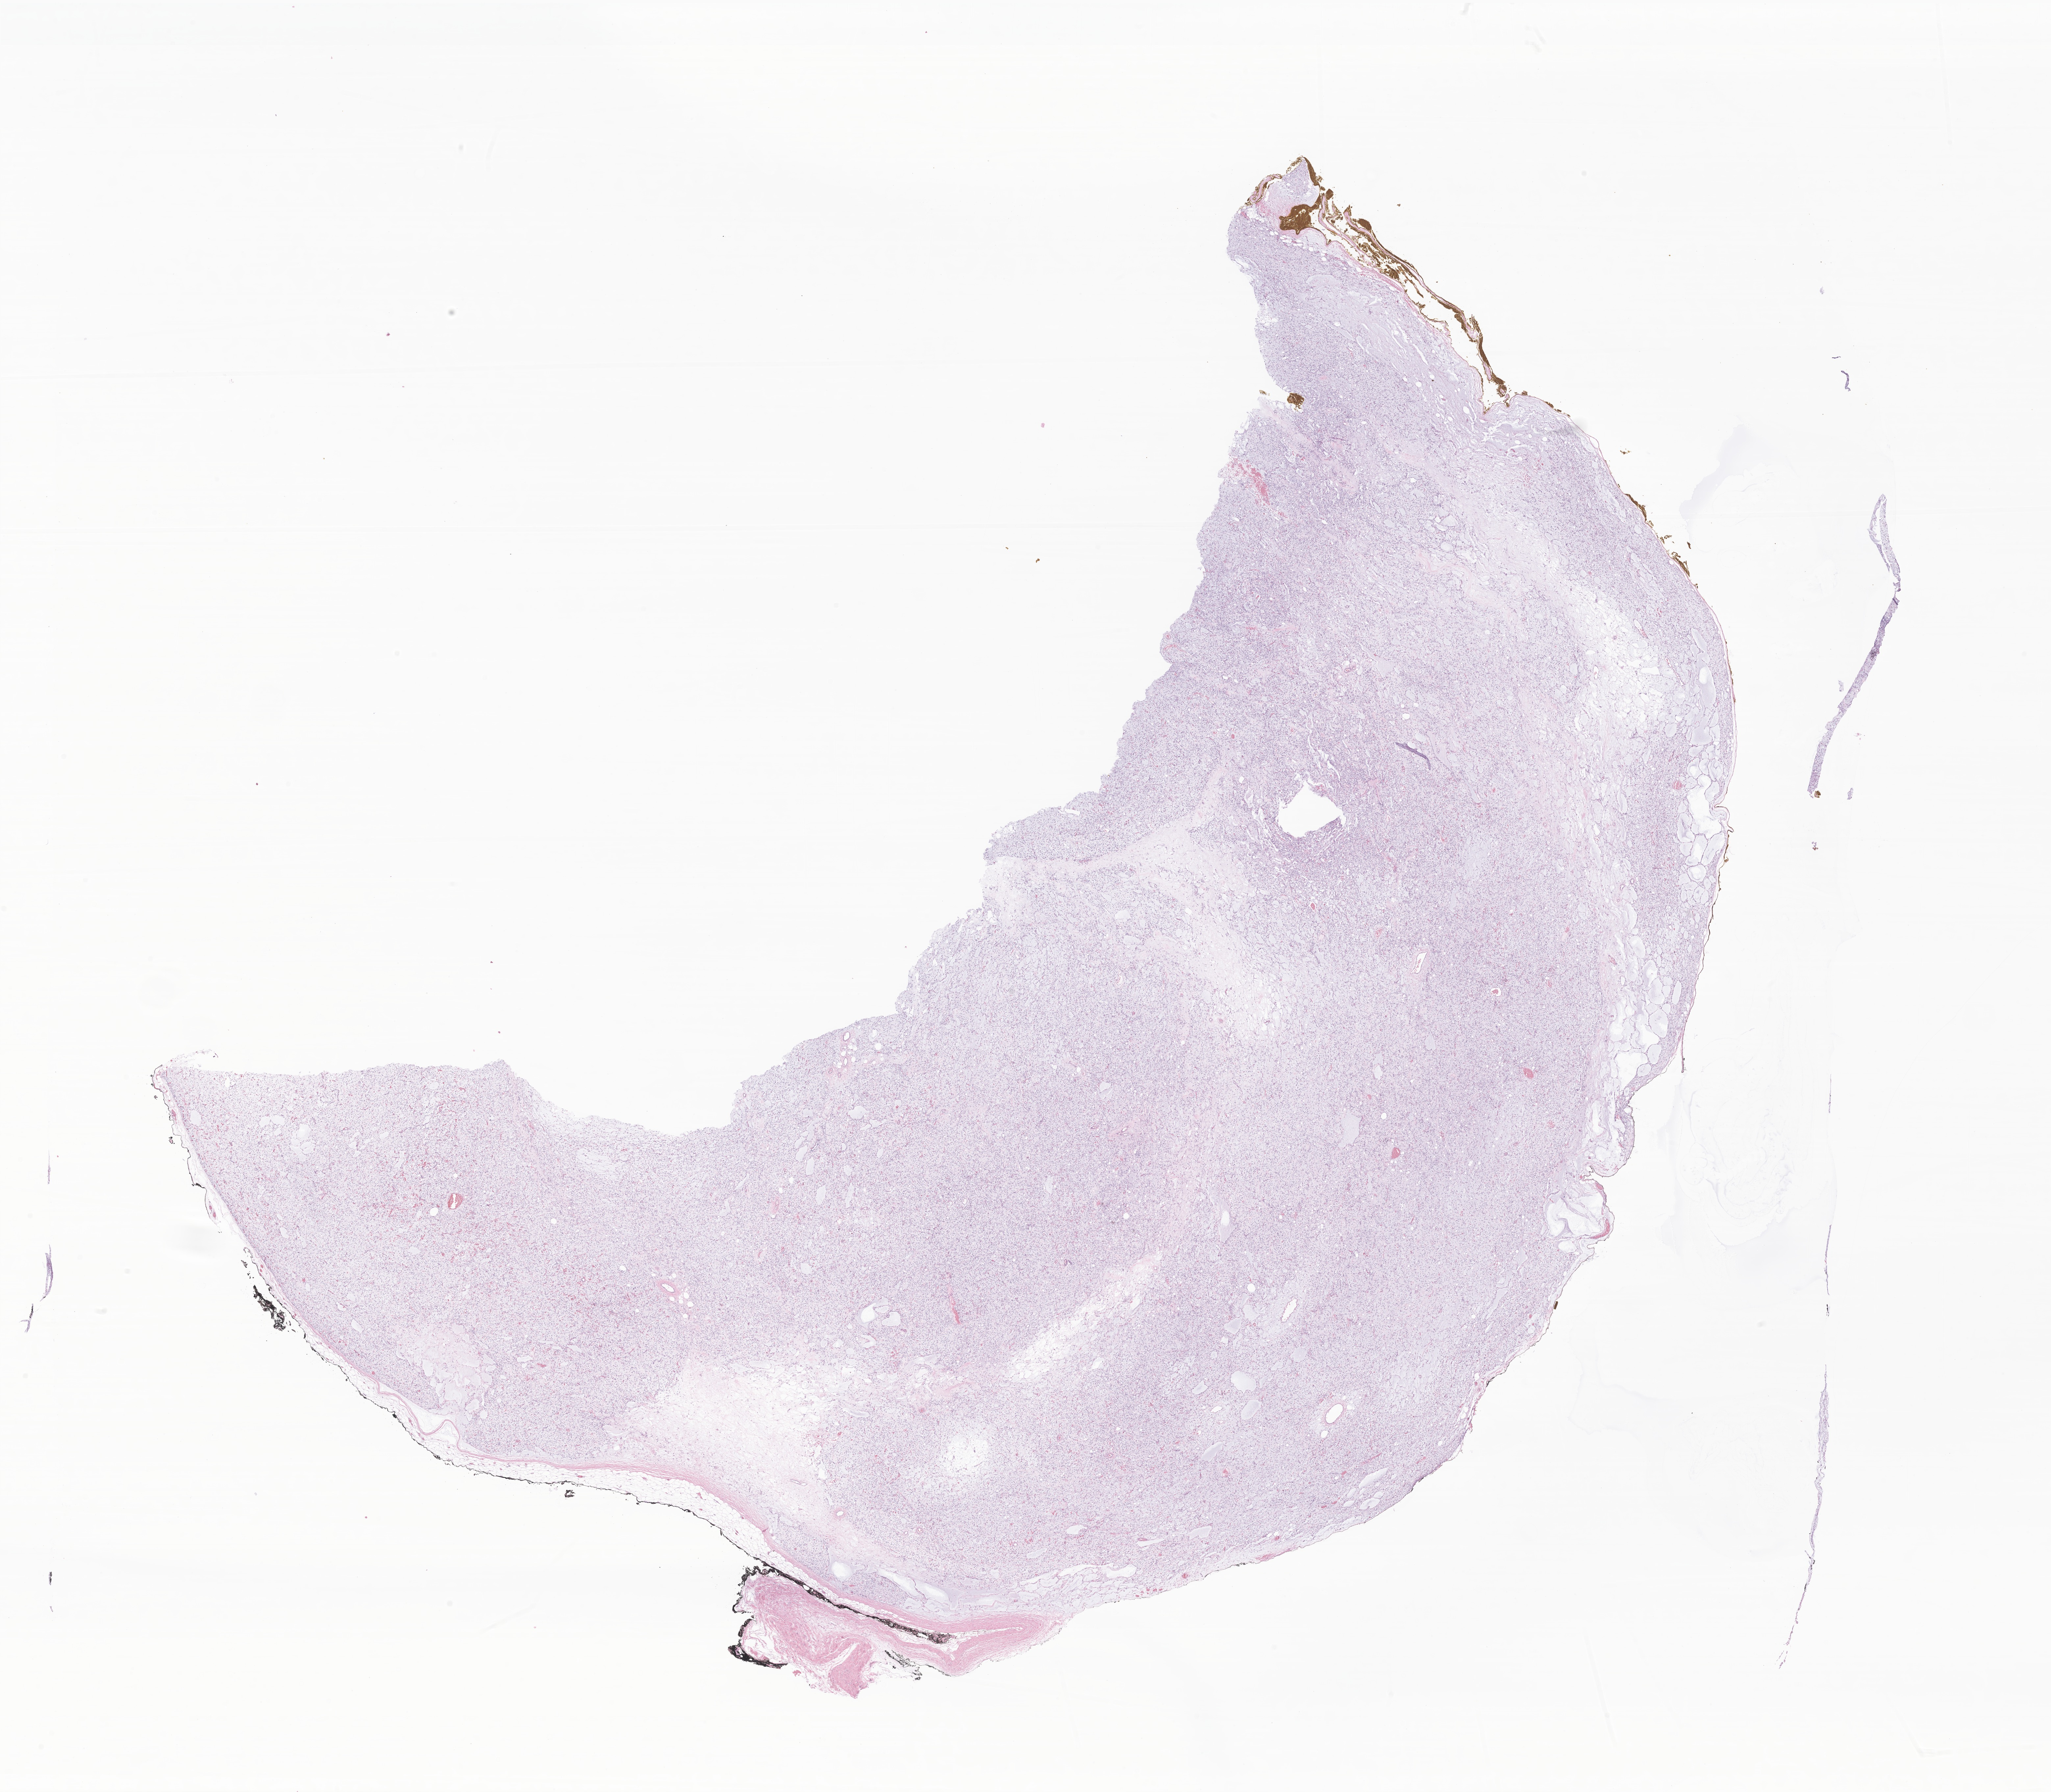
Digitized H&E-stained section of tumor tissue from the soft tissue of lower extremity, shown as a low-resolution overview of the whole scanned area (about 26.3 x 23.0 mm). FFPE section. Patient female; age 217 months (18 years 1 month).
Diagnosis (ICD-O-3 morphology term): Myxoid liposarcoma.